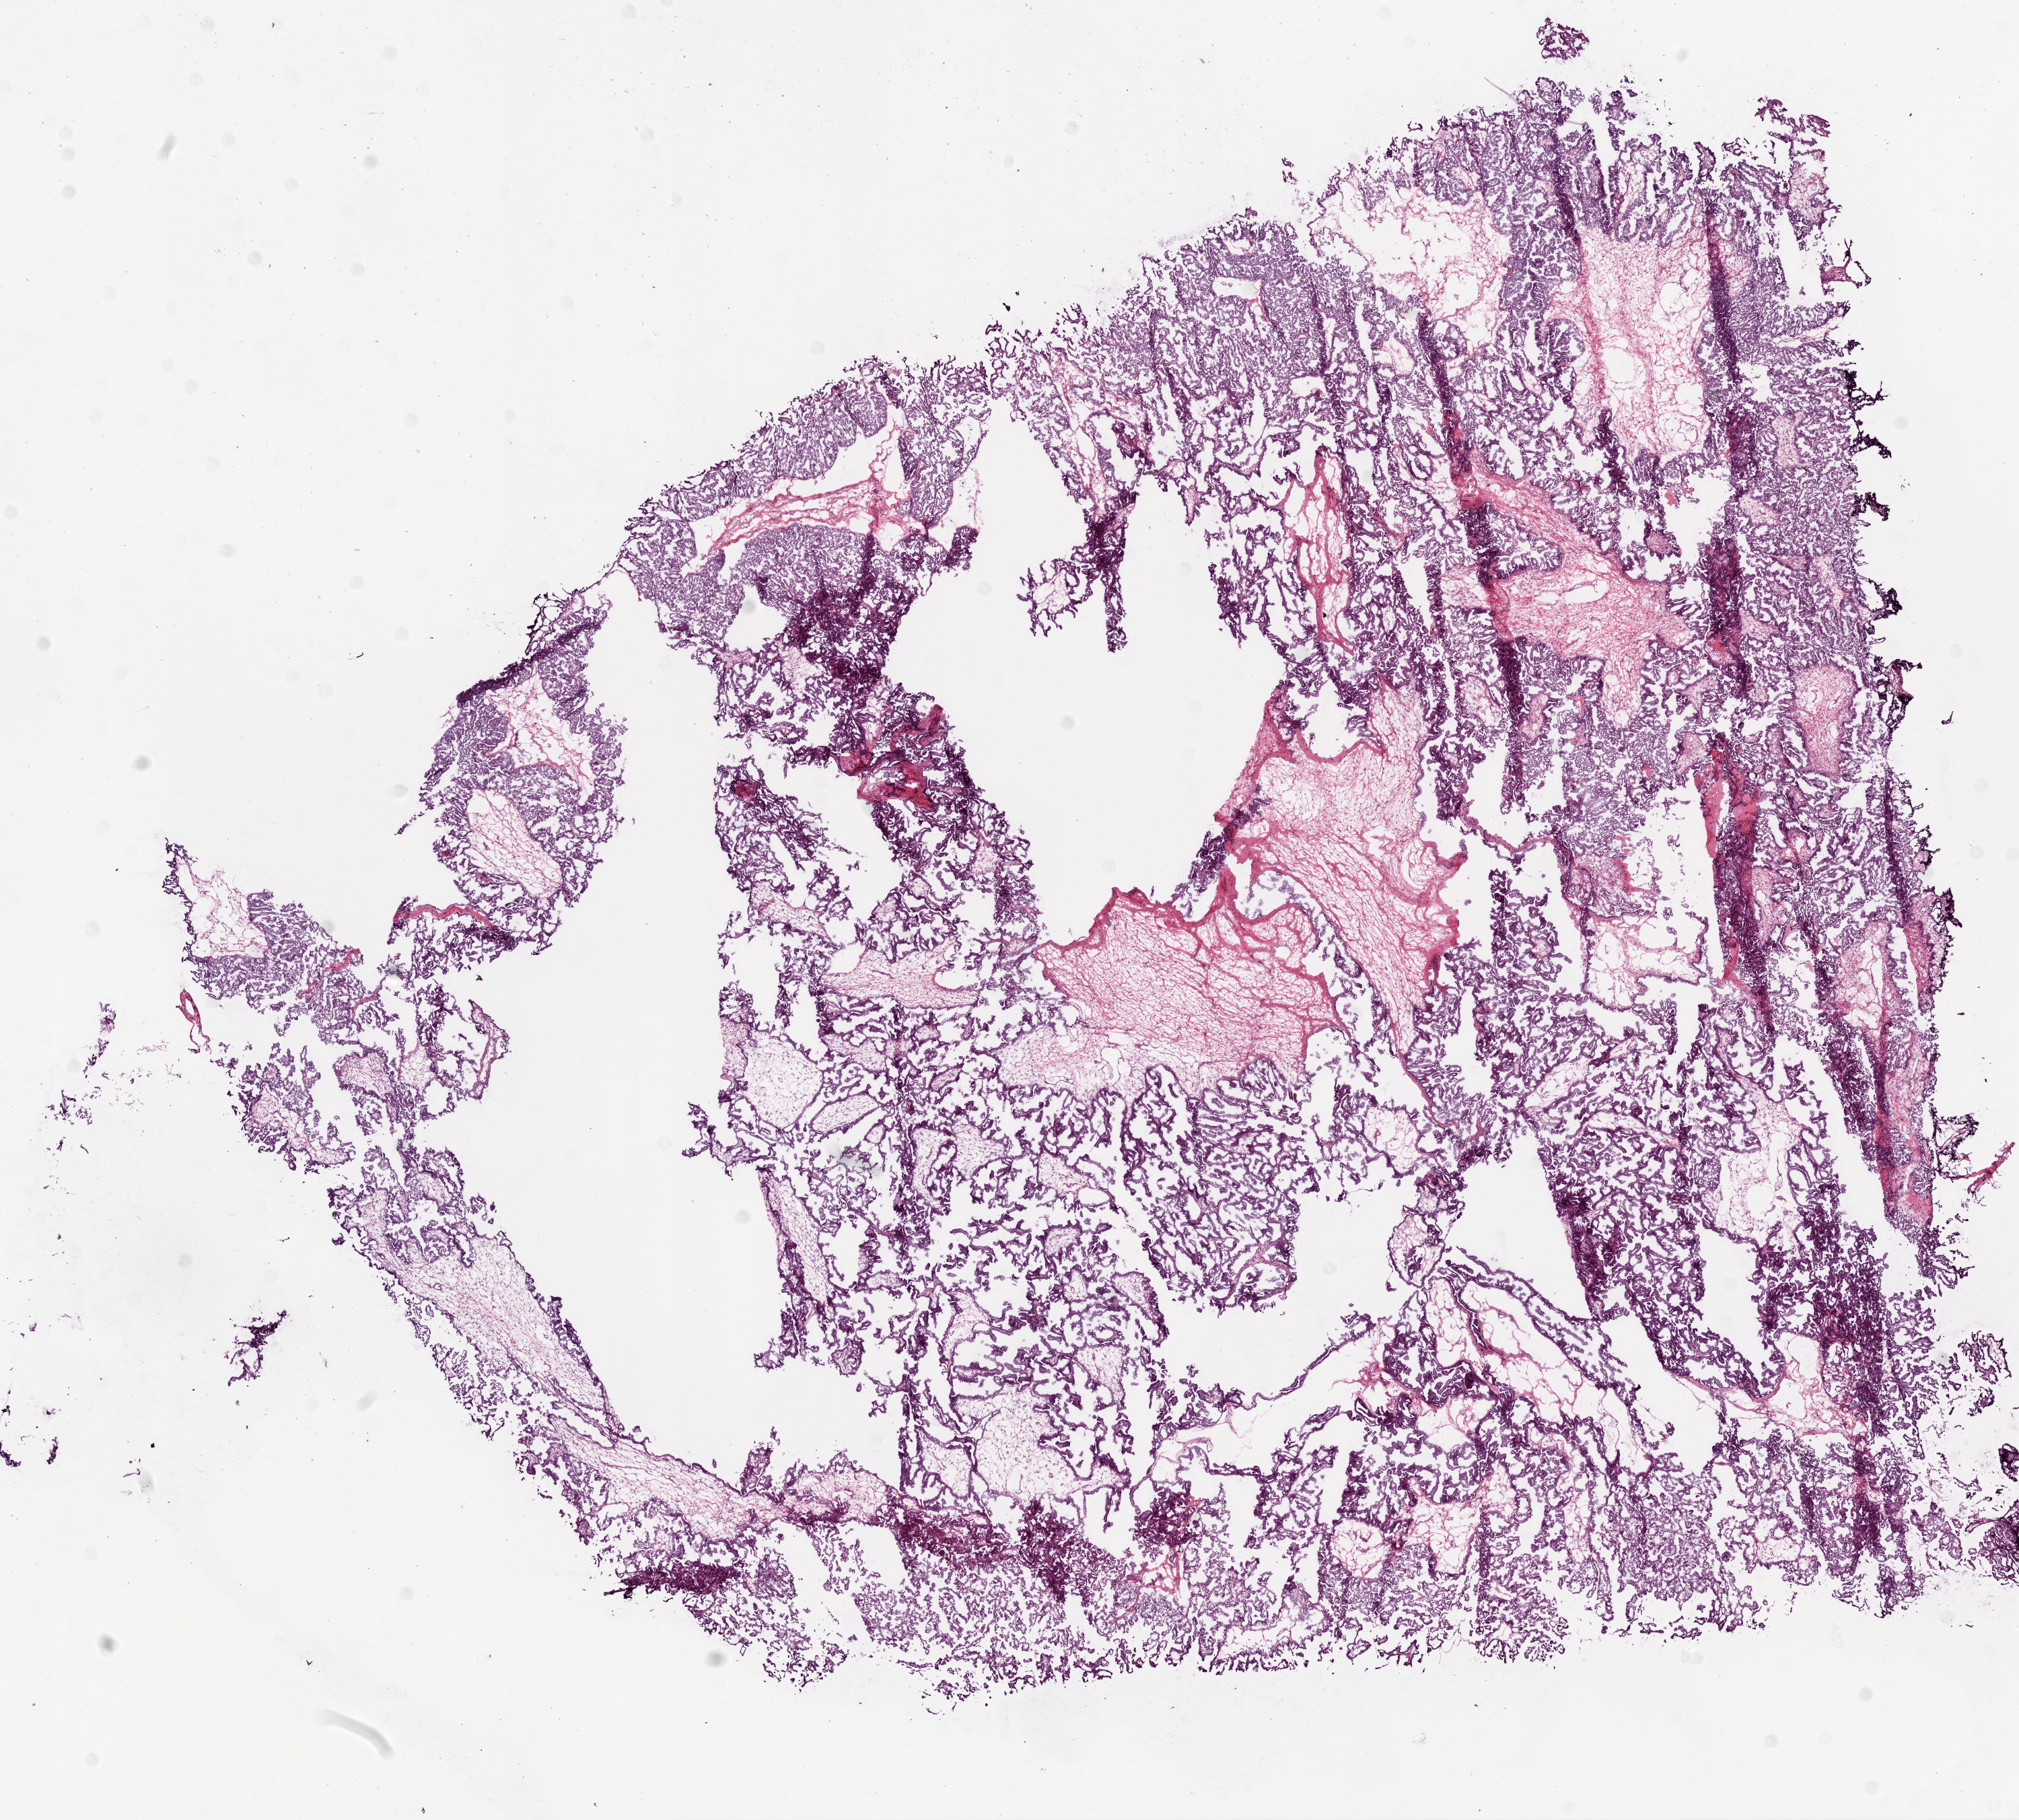
Whole-slide histology image, Hematoxylin and eosin (H&E) stained, a low-resolution overview of the entire scanned area, about 12.0 x 10.8 mm. Frozen section from the bottom of the tissue portion. Ovary, primary tumour sample. Female, age 43 years at initial diagnosis. Histologic grade: G2 (moderately differentiated). Pathologist review of this section (percent, as recorded): tumour cells 100%, tumour nuclei 70%, normal cells 0%, stromal cells 0%, necrosis 0%.
Laterality: right. Diagnosis: Serous cystadenocarcinoma, NOS. FIGO stage: IIIC.